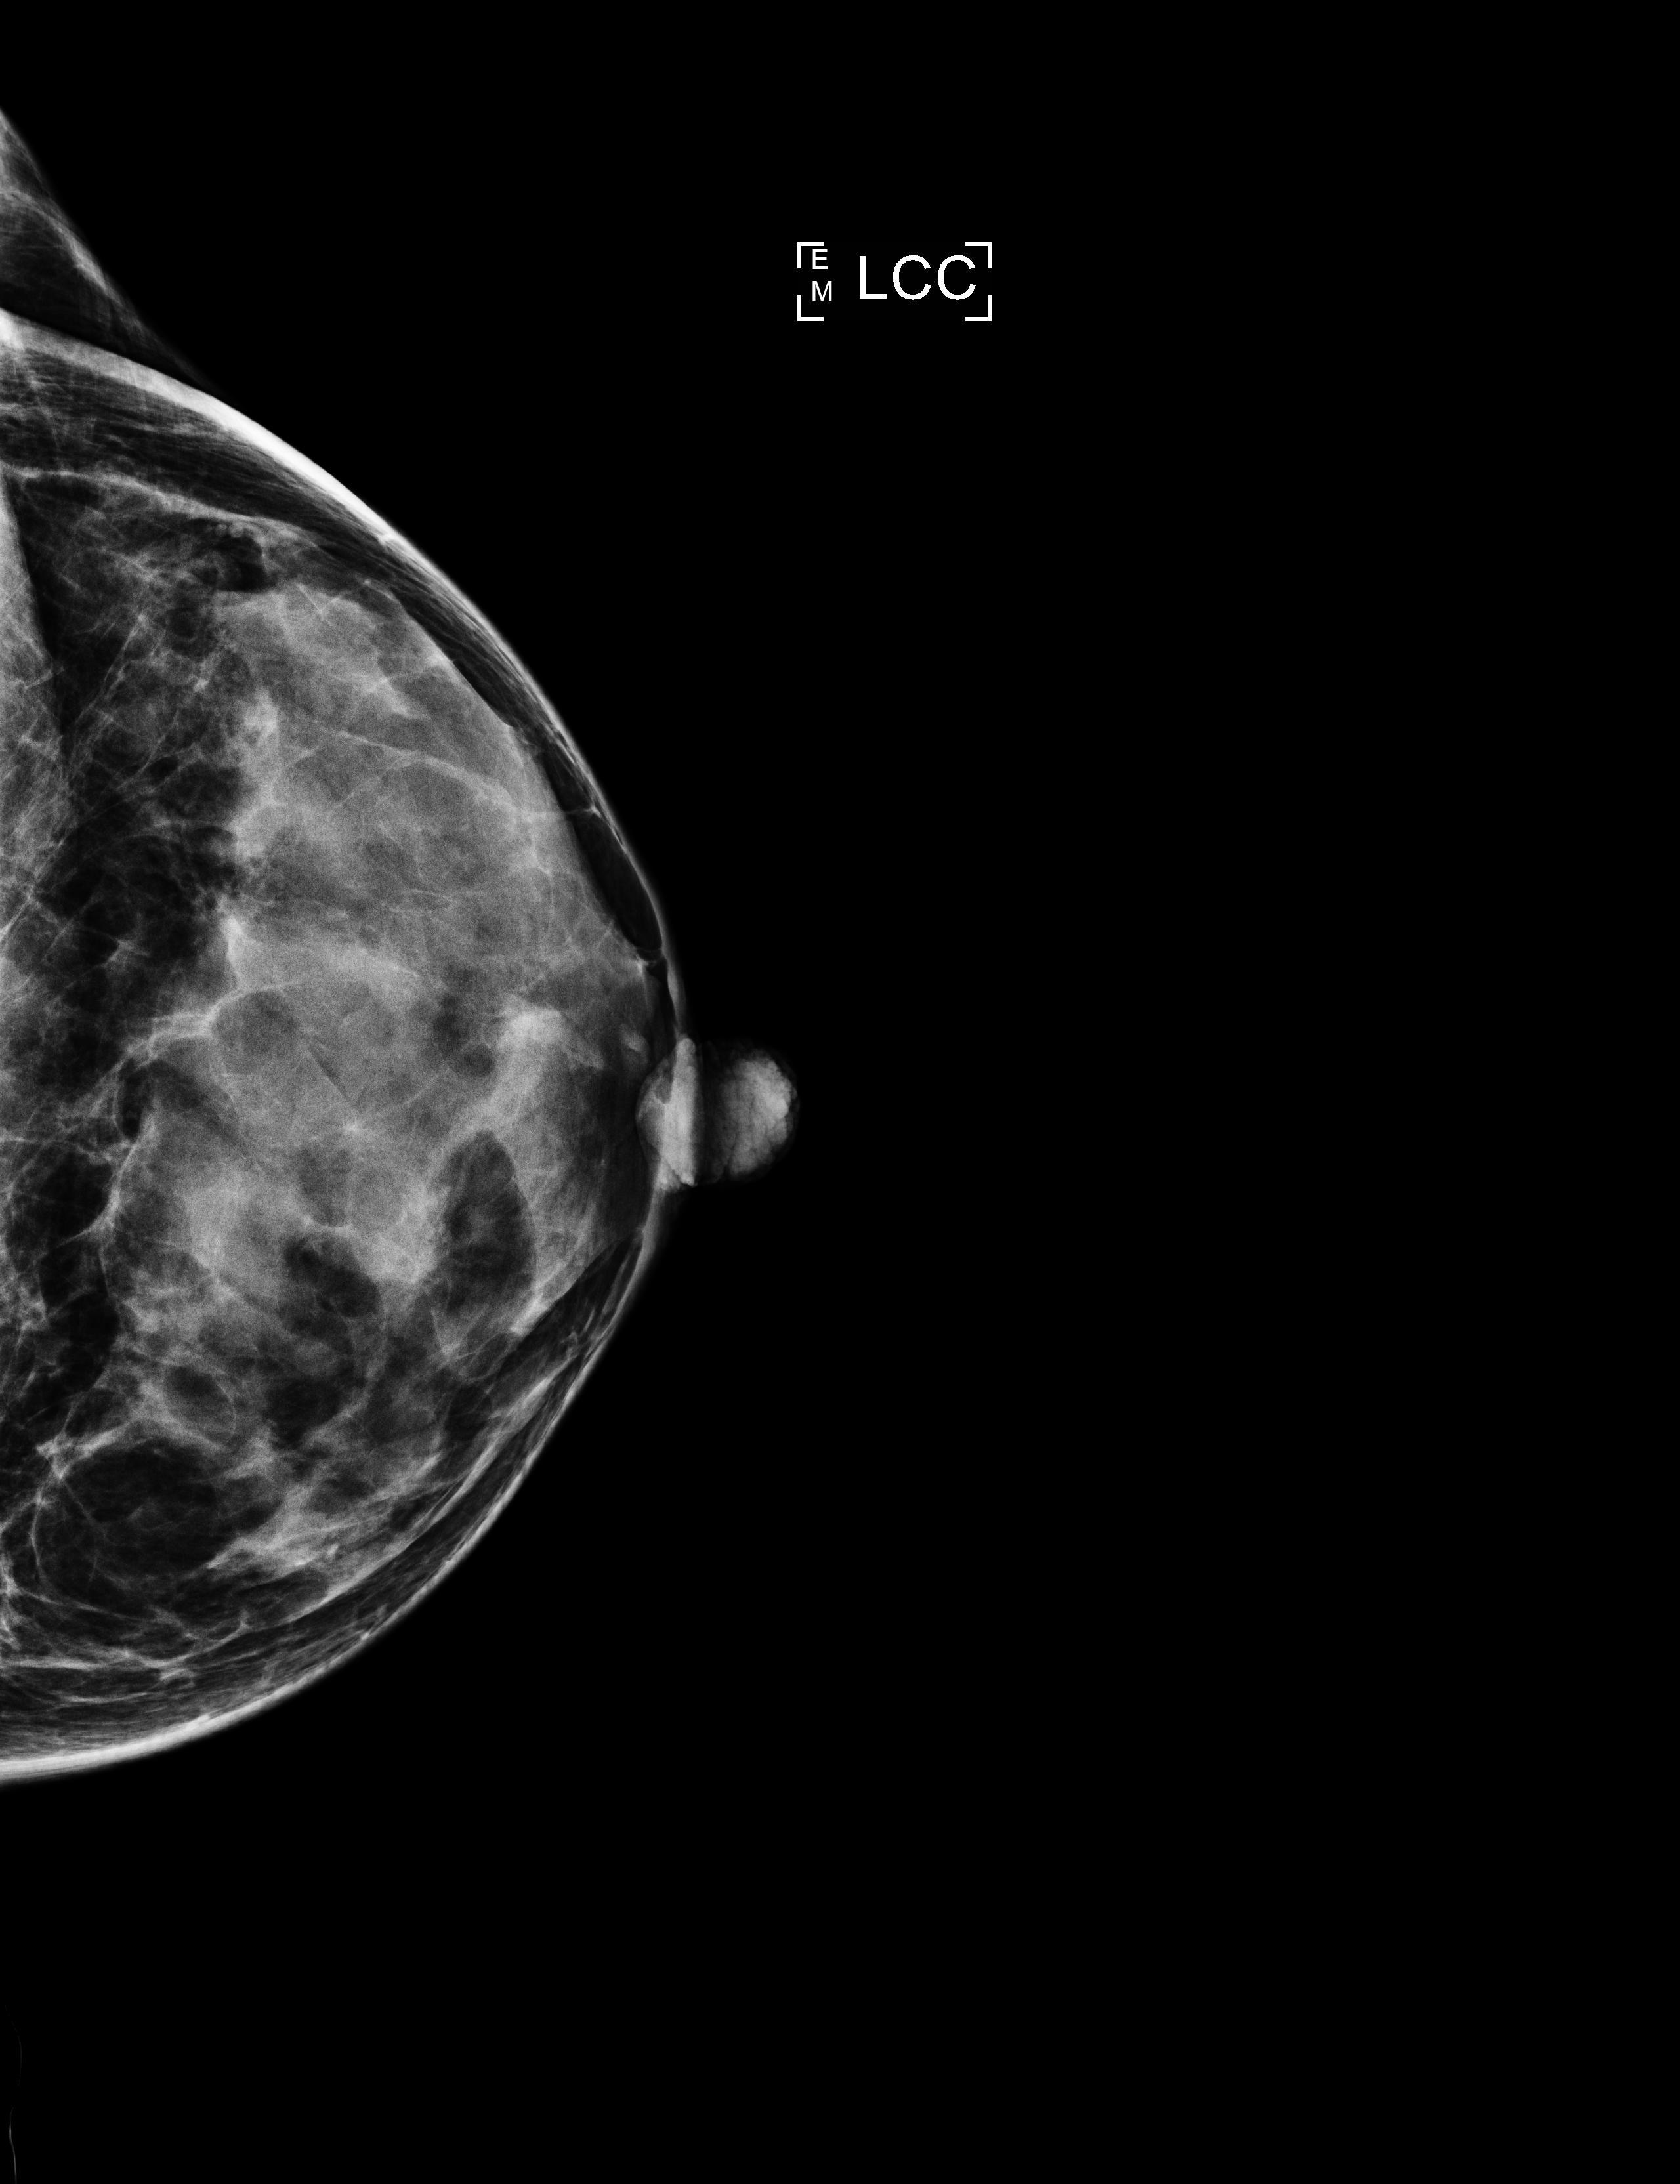
Screening examination, compressed breast thickness 44 mm, system: Selenia Dimensions. Female patient, age 42 years.
Image type: full-field digital mammogram. Breast: left. Projection: cranio-caudal projection. BI-RADS breast density category at the screening exam (both breasts, scale 1–4): 4. Final BI-RADS category for the screening round (tomosynthesis exam, both breasts): category 2. Recall: recalled for additional imaging after this screen.